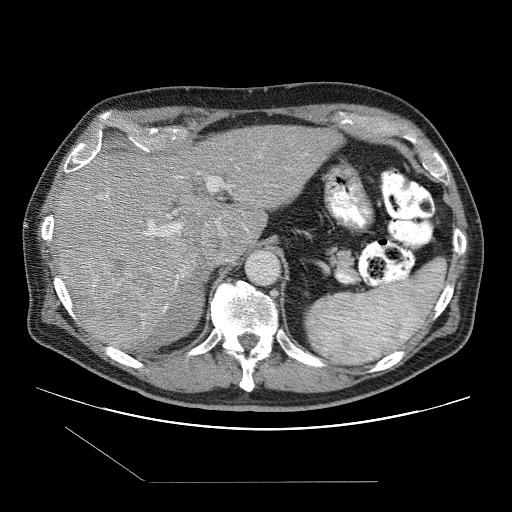
Contrast-enhanced abdominal CT (liver protocol), one axial slice. Slice 69 of 109 in the series (ordered by position). Reconstruction kernel STANDARD. 120 kVp. One of 2 acquisitions stored at this slice position. Soft-tissue window (W 400 / L 40 HU). 2.5 mm slice thickness. 512 × 512 image matrix. Case-level facts recorded for this patient, not image findings: diagnosis: hepatocellular carcinoma (patient treated with transarterial chemoembolisation; whether this scan precedes or follows treatment is not stated here); TNM stage (as recorded): Stage-IIIB; Child-Pugh class: A; tumour differentiation: well differentiated.
Annotated regions visible in this slice (semi-automatic segmentation, software-assisted and operator-edited):
- abdominal aorta: bounding box <246,250,279,285> (left, top, right, bottom; pixels)
- liver parenchyma outside the tumour (the mass and vessels are separate outlines, so this box may not span the whole liver): <56,126,342,348>
- mass: <59,240,190,349>
- liver vessels: <86,172,218,310>